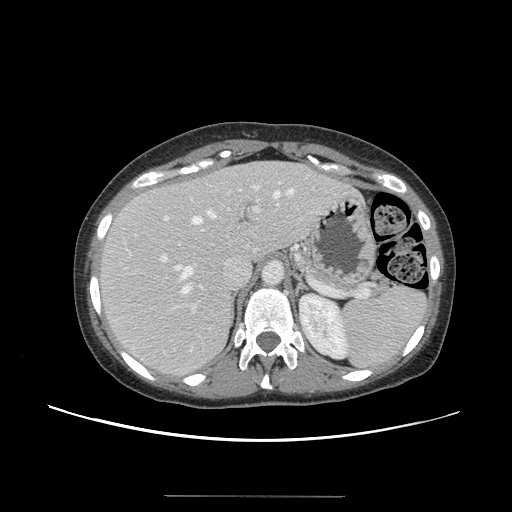
Contrast-enhanced abdominal CT, one axial slice; slice 101 of 144 in the series (ordered by position); intravenous contrast given; soft-tissue window (W 400 / L 40 HU); 2.5 mm slice thickness; 512 × 512 image matrix, field of view 380 × 380 mm. Female patient, age 53 years. From the clinical record (not read from this slice): diagnosis: colorectal cancer liver metastases, imaged before liver resection; multiple liver metastases: yes; largest metastasis: 1.1 cm.
Outlined on this slice (expert manual segmentation):
- hepatic veins: bounding box [x1, y1, x2, y2] px = [176, 186, 293, 293]
- liver: [100, 162, 355, 376]
- planned liver remnant (the part of the liver to remain after resection): [100, 163, 304, 300]
- portal vein (with intrahepatic branches): [160, 181, 281, 312]